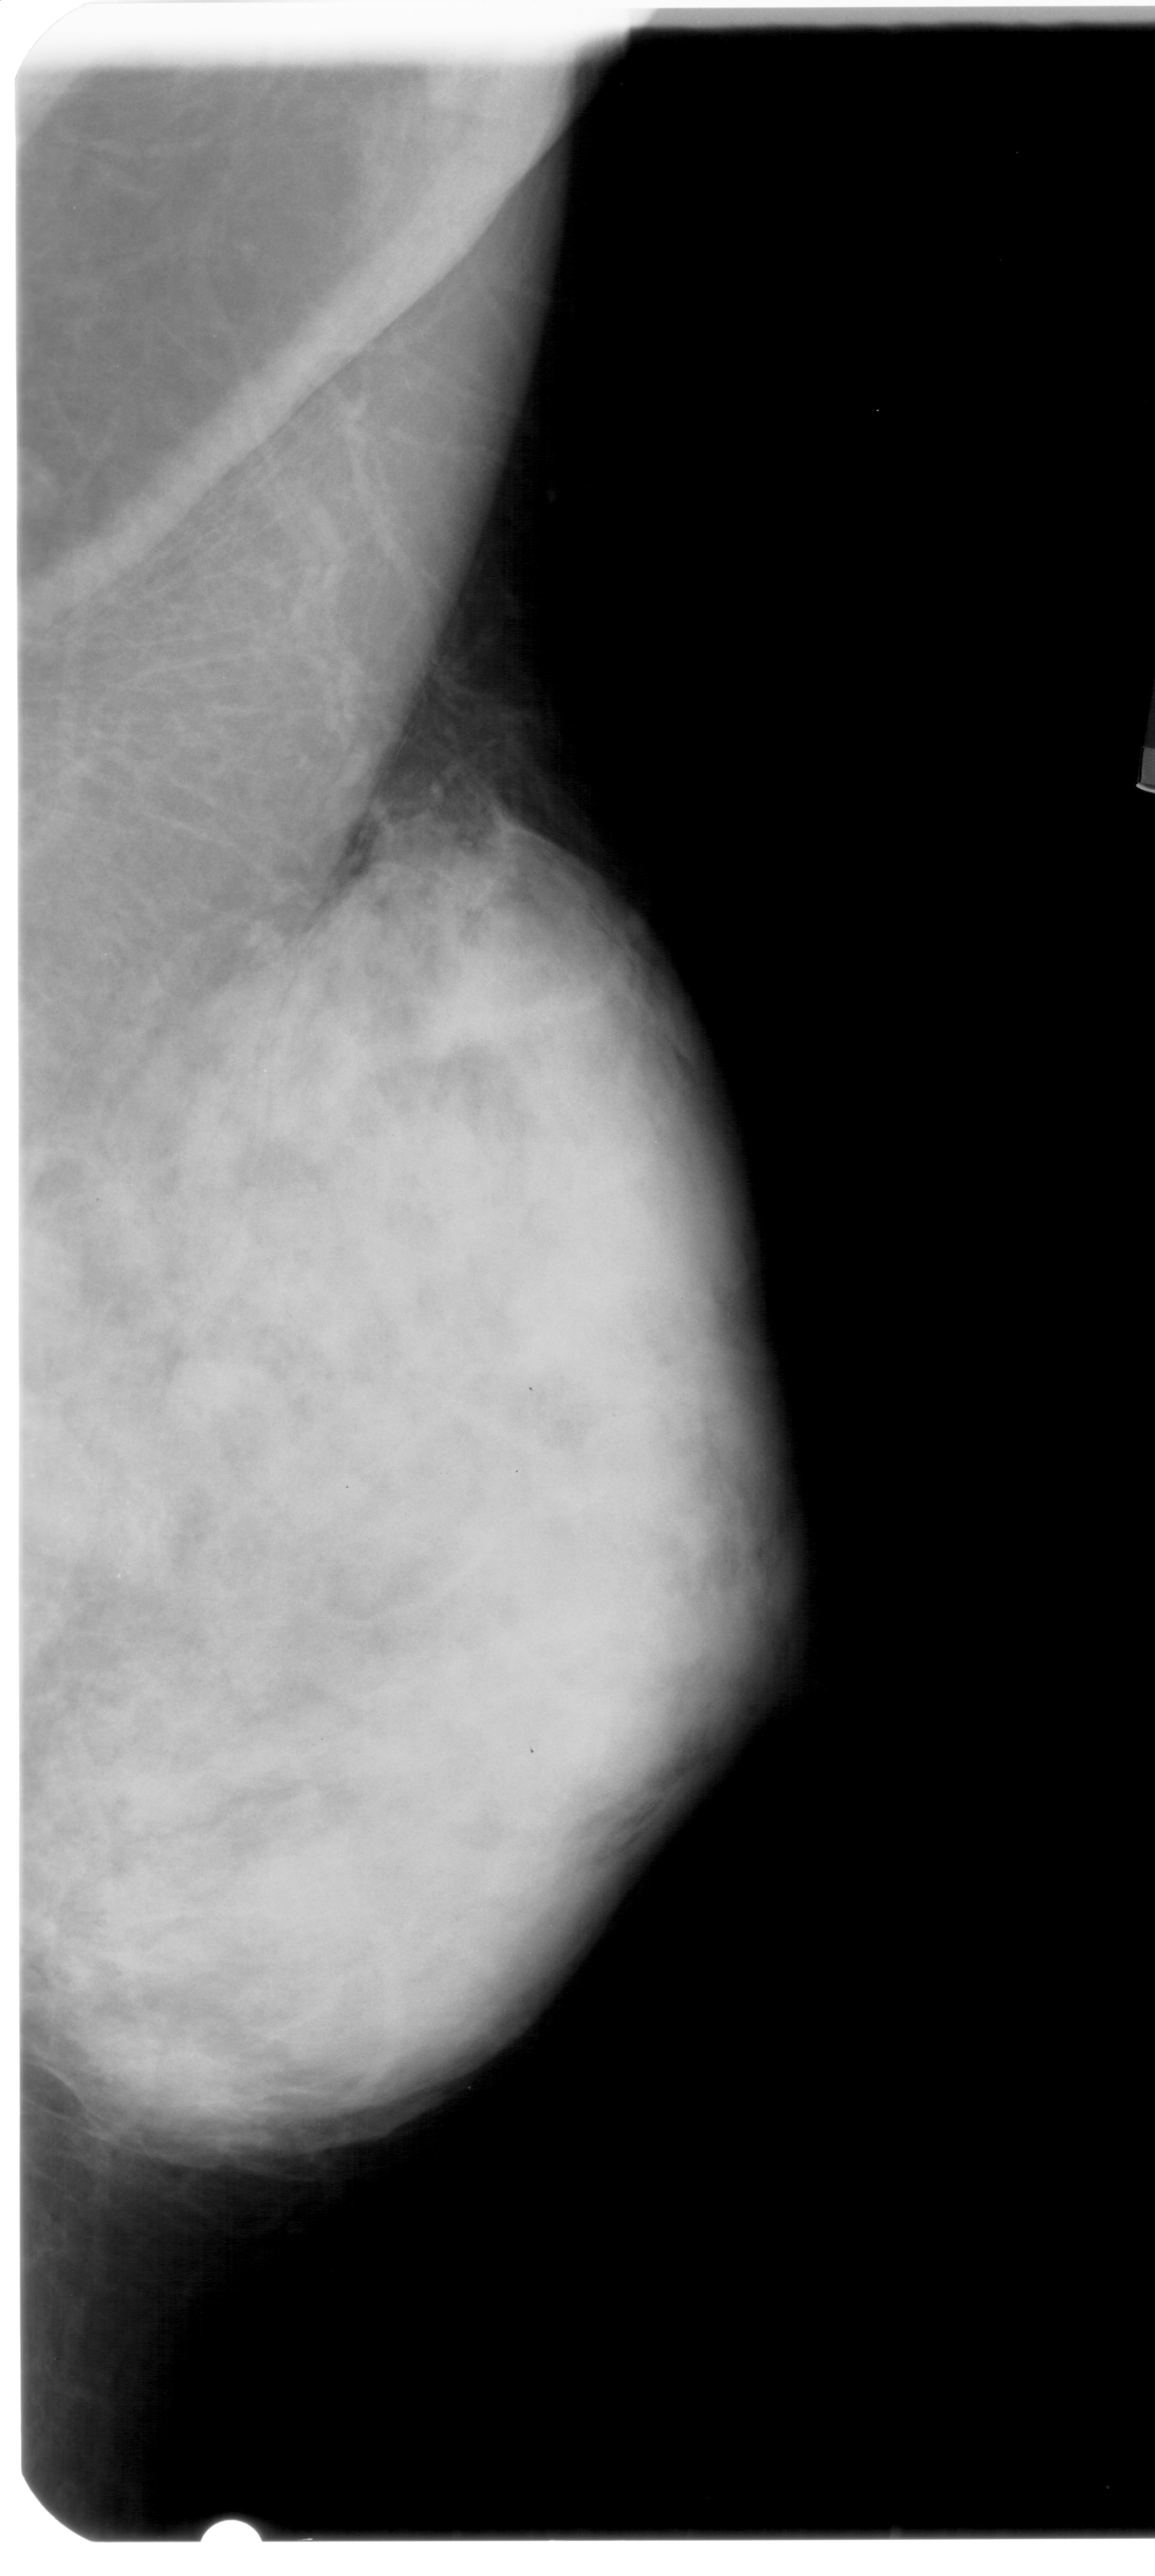
Digitized screen-film mammogram. Right breast. Mediolateral oblique (MLO) view. BI-RADS breast density category 4 (scale 1–4). 1155 × 2576 image matrix.
Expert-marked regions of interest on this film, with their recorded descriptors:
- calcifications, morphology pleomorphic, distribution clustered; BI-RADS assessment category 4; pathology (as recorded): benign: bounding box <20,1394,157,1643> (left, top, right, bottom; pixels)